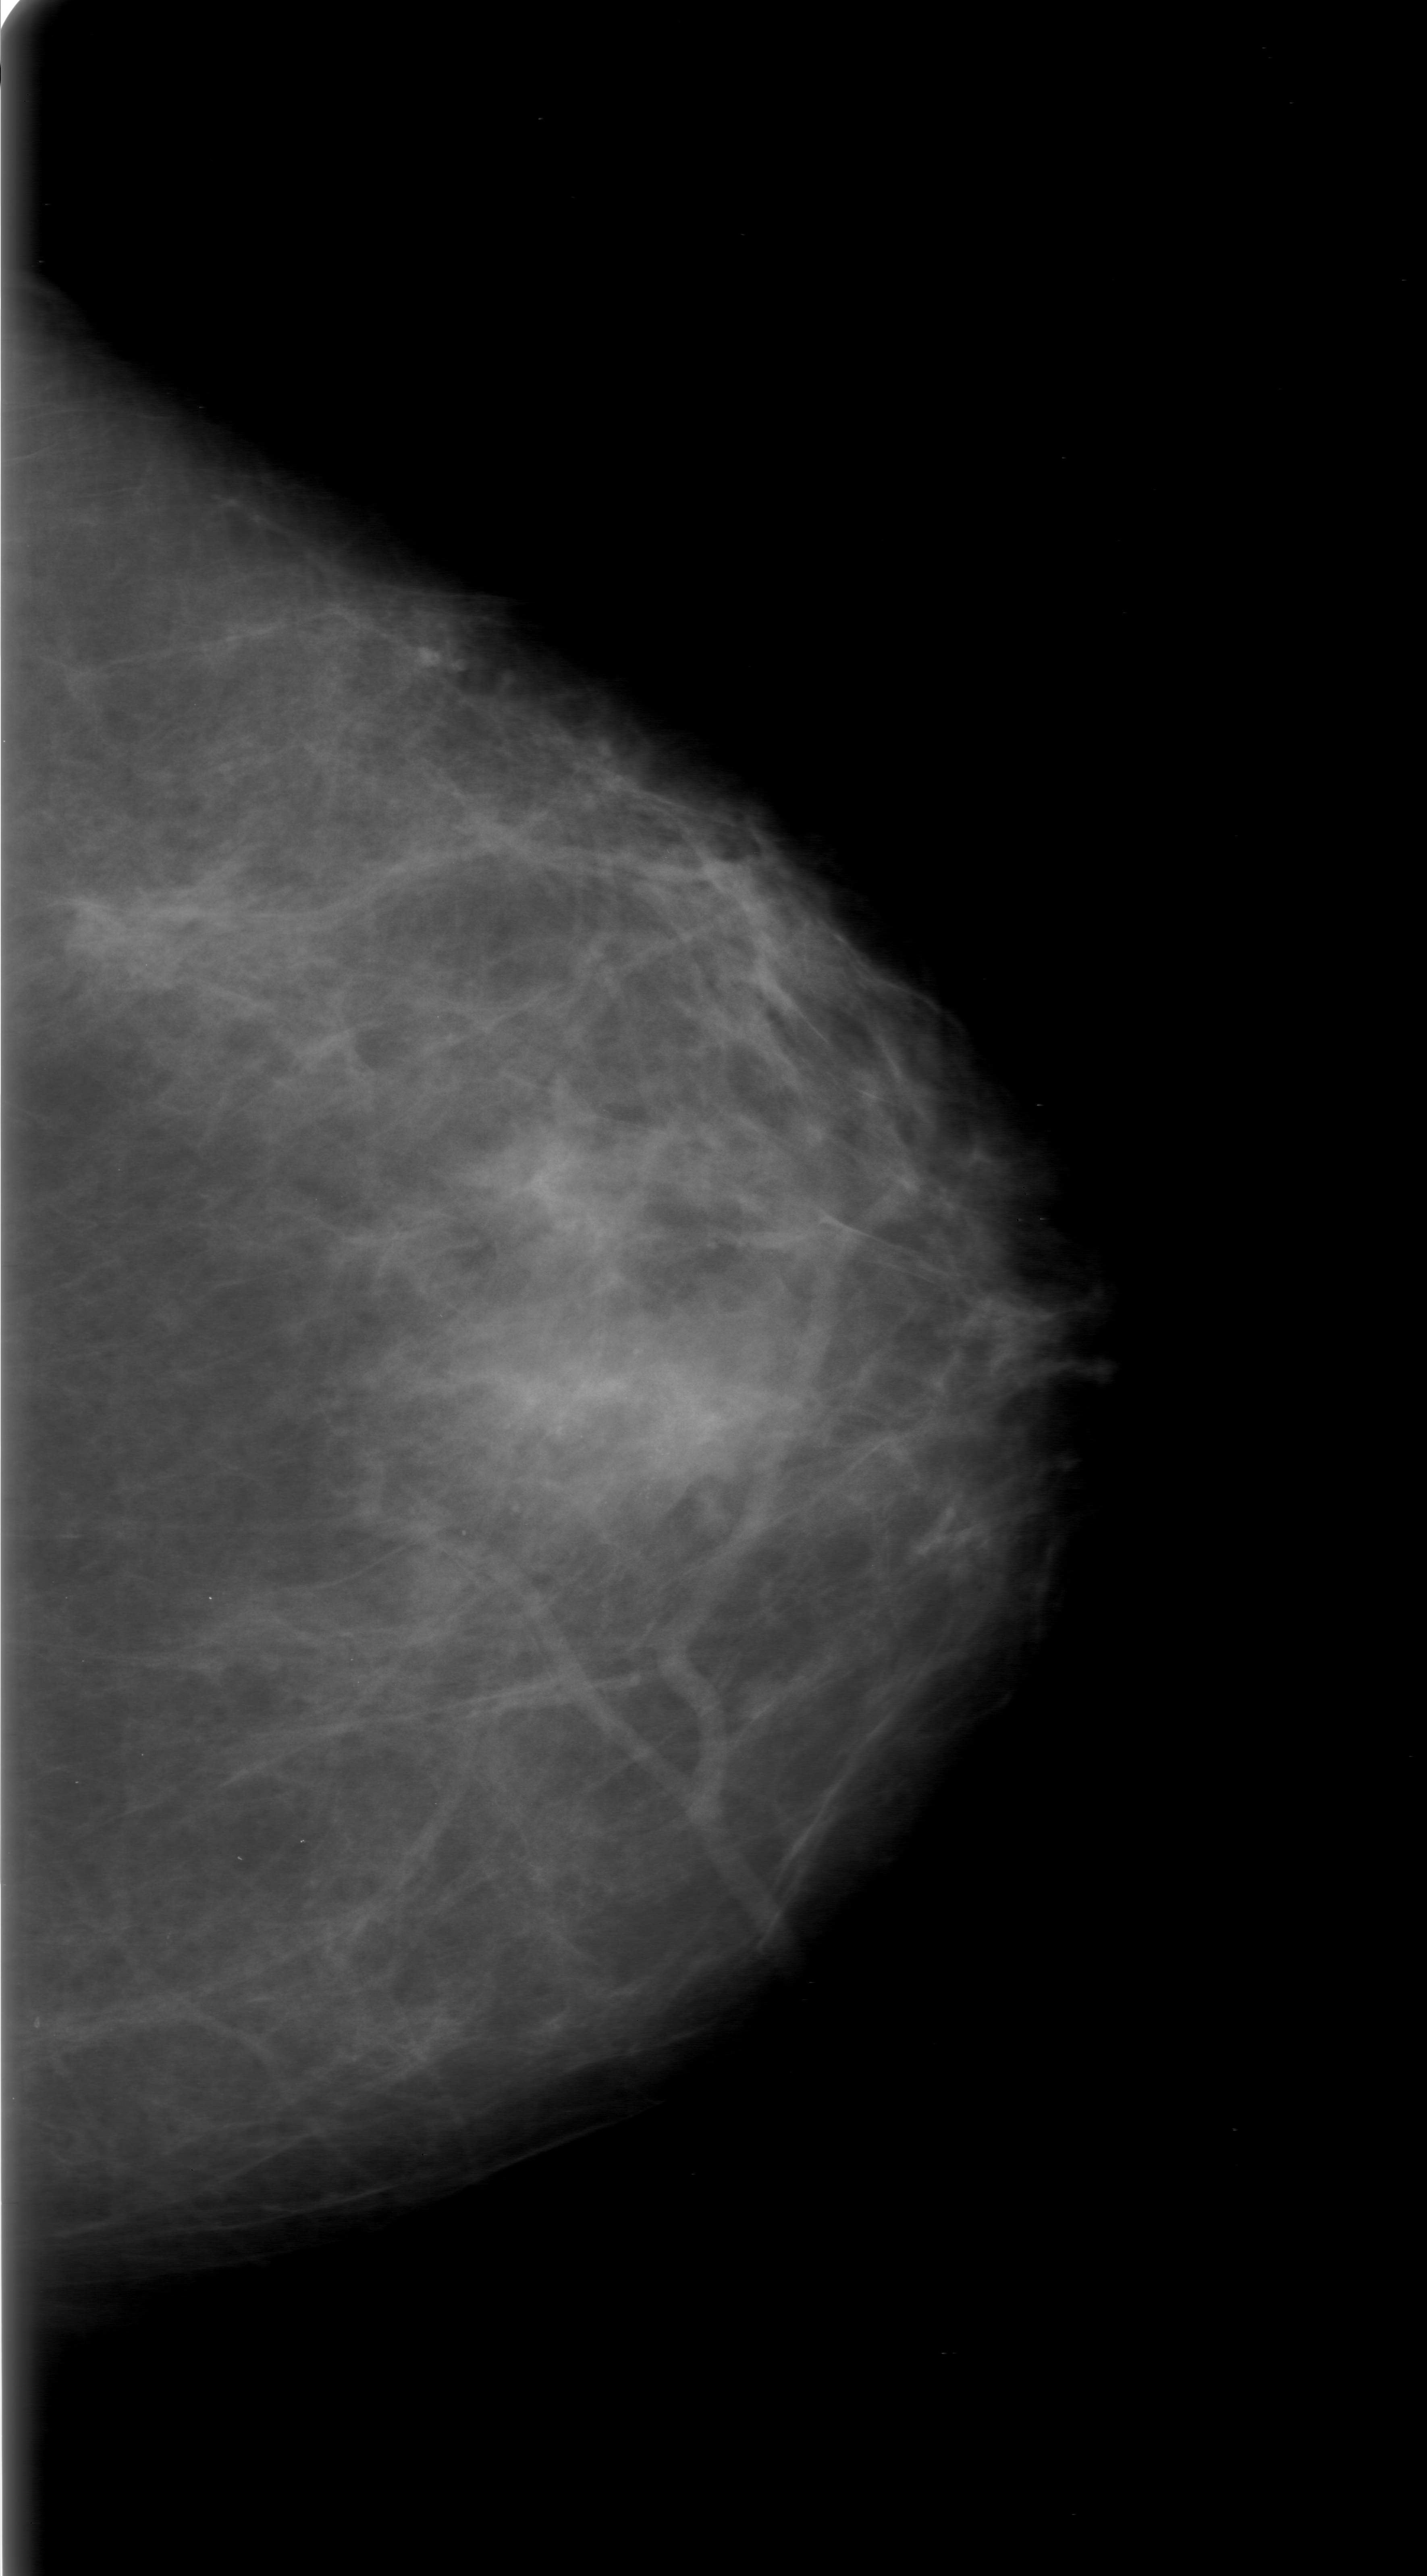
Scanned film-screen mammogram, left breast, CC view, BI-RADS breast density category 2 (scale 1–4).
Marked findings (only marked abnormalities are described; nothing is implied about the rest of the image): calcifications, morphology amorphous, distribution clustered; BI-RADS assessment category 0 (incomplete: needs additional imaging); subtlety rating 2 on a 1 (subtle) to 5 (obvious) scale; pathology result (as recorded, not read from the image): malignant.